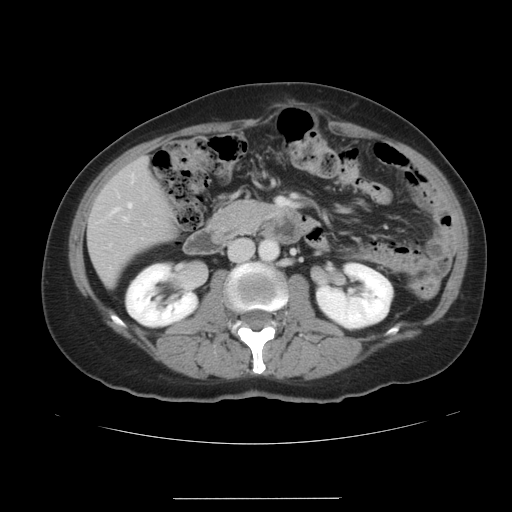
Contrast-enhanced abdominal CT, one axial slice. Position 13 of 41 along the scan axis. 120 kVp. Intravenous contrast given. Soft-tissue window (W 400 / L 40 HU). 5 mm slice thickness. 512 × 512 image matrix, field of view 381 × 381 mm. Female patient, age 63 years. From the clinical record (not read from this slice): diagnosis: colorectal cancer liver metastases, imaged before liver resection; multiple liver metastases: yes; largest metastasis: 1.5 cm; disease in both lobes: yes.
Annotated regions visible in this slice (expert manual segmentation):
- hepatic veins: bounding box <113,203,131,213> (left, top, right, bottom; pixels)
- liver: <89,160,176,286>
- planned liver remnant (the part of the liver to remain after resection): <89,171,176,286>
- portal vein (with intrahepatic branches): <124,217,128,221>